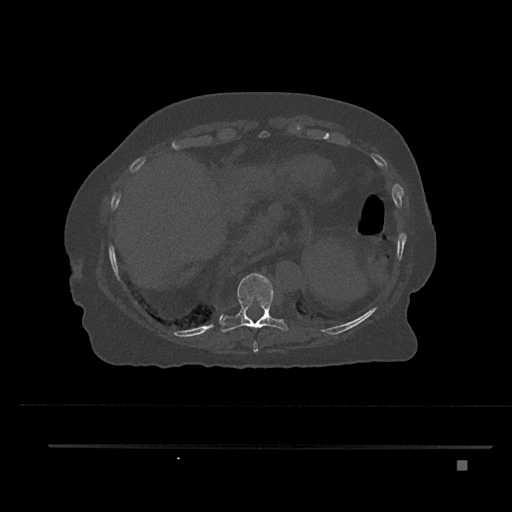
CT including the spine, one axial slice; position 358 of 797 along the scan axis; reconstruction kernel Br40s/3; bone window (W 1800 / L 400 HU); 0.5 mm slice thickness; 512 × 512 image matrix, field of view 437 × 437 mm. Female patient, age 76 years. From the clinical record (not read from this slice): primary cancer: lung; vertebrae with lytic lesions (as recorded): T11, L3.
Outlined on this slice (semi-automatic segmentation, software-assisted and operator-edited):
- T10 vertebra: box from (x=220, y=273) to (x=289, y=333) px
- T9 vertebra: (x=253, y=340)–(x=259, y=353)